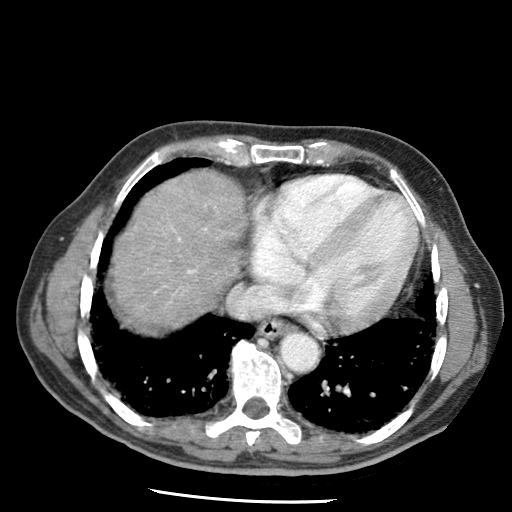
Contrast-enhanced abdominal CT (liver protocol), one axial slice; position 62 of 79 along the scan axis; soft-tissue window (W 400 / L 40 HU); 512 × 512 image matrix, field of view 320 × 320 mm. Case-level facts recorded for this patient, not image findings: diagnosis: hepatocellular carcinoma (patient treated with transarterial chemoembolisation; whether this scan precedes or follows treatment is not stated here); TNM stage (as recorded): Stage-IIIA; Child-Pugh class: A; tumour differentiation: moderately differentiated; tumour nodularity: multinodular.
Outlined on this slice (semi-automatically segmented with operator editing):
- liver parenchyma outside the tumour (the mass and vessels are separate outlines, so this box may not span the whole liver): bounding box <112,172,246,328> (left, top, right, bottom; pixels)
- liver vessels: <154,190,216,303>